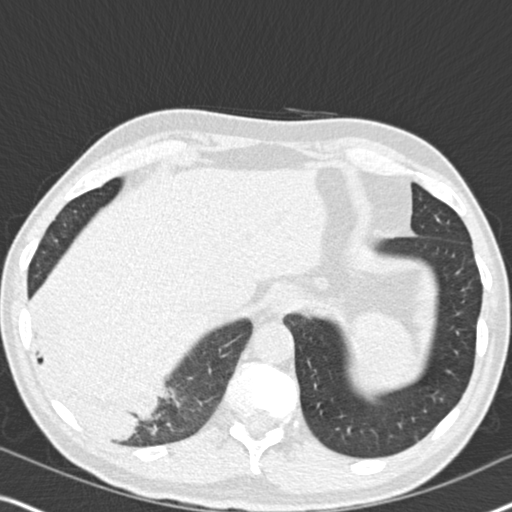
Low-dose screening chest CT, one axial slice; position 49 of 182 along the scan axis; 120 kVp; lung window (W 1500 / L -600 HU); 512 × 512 image matrix, field of view 330 × 330 mm.
Annotated regions visible in this slice (manually delineated by an expert):
- lesion 1 (tumor, lower lobe of right lung): bounding box (x1, y1, x2, y2) in pixels: (64, 387, 152, 436)